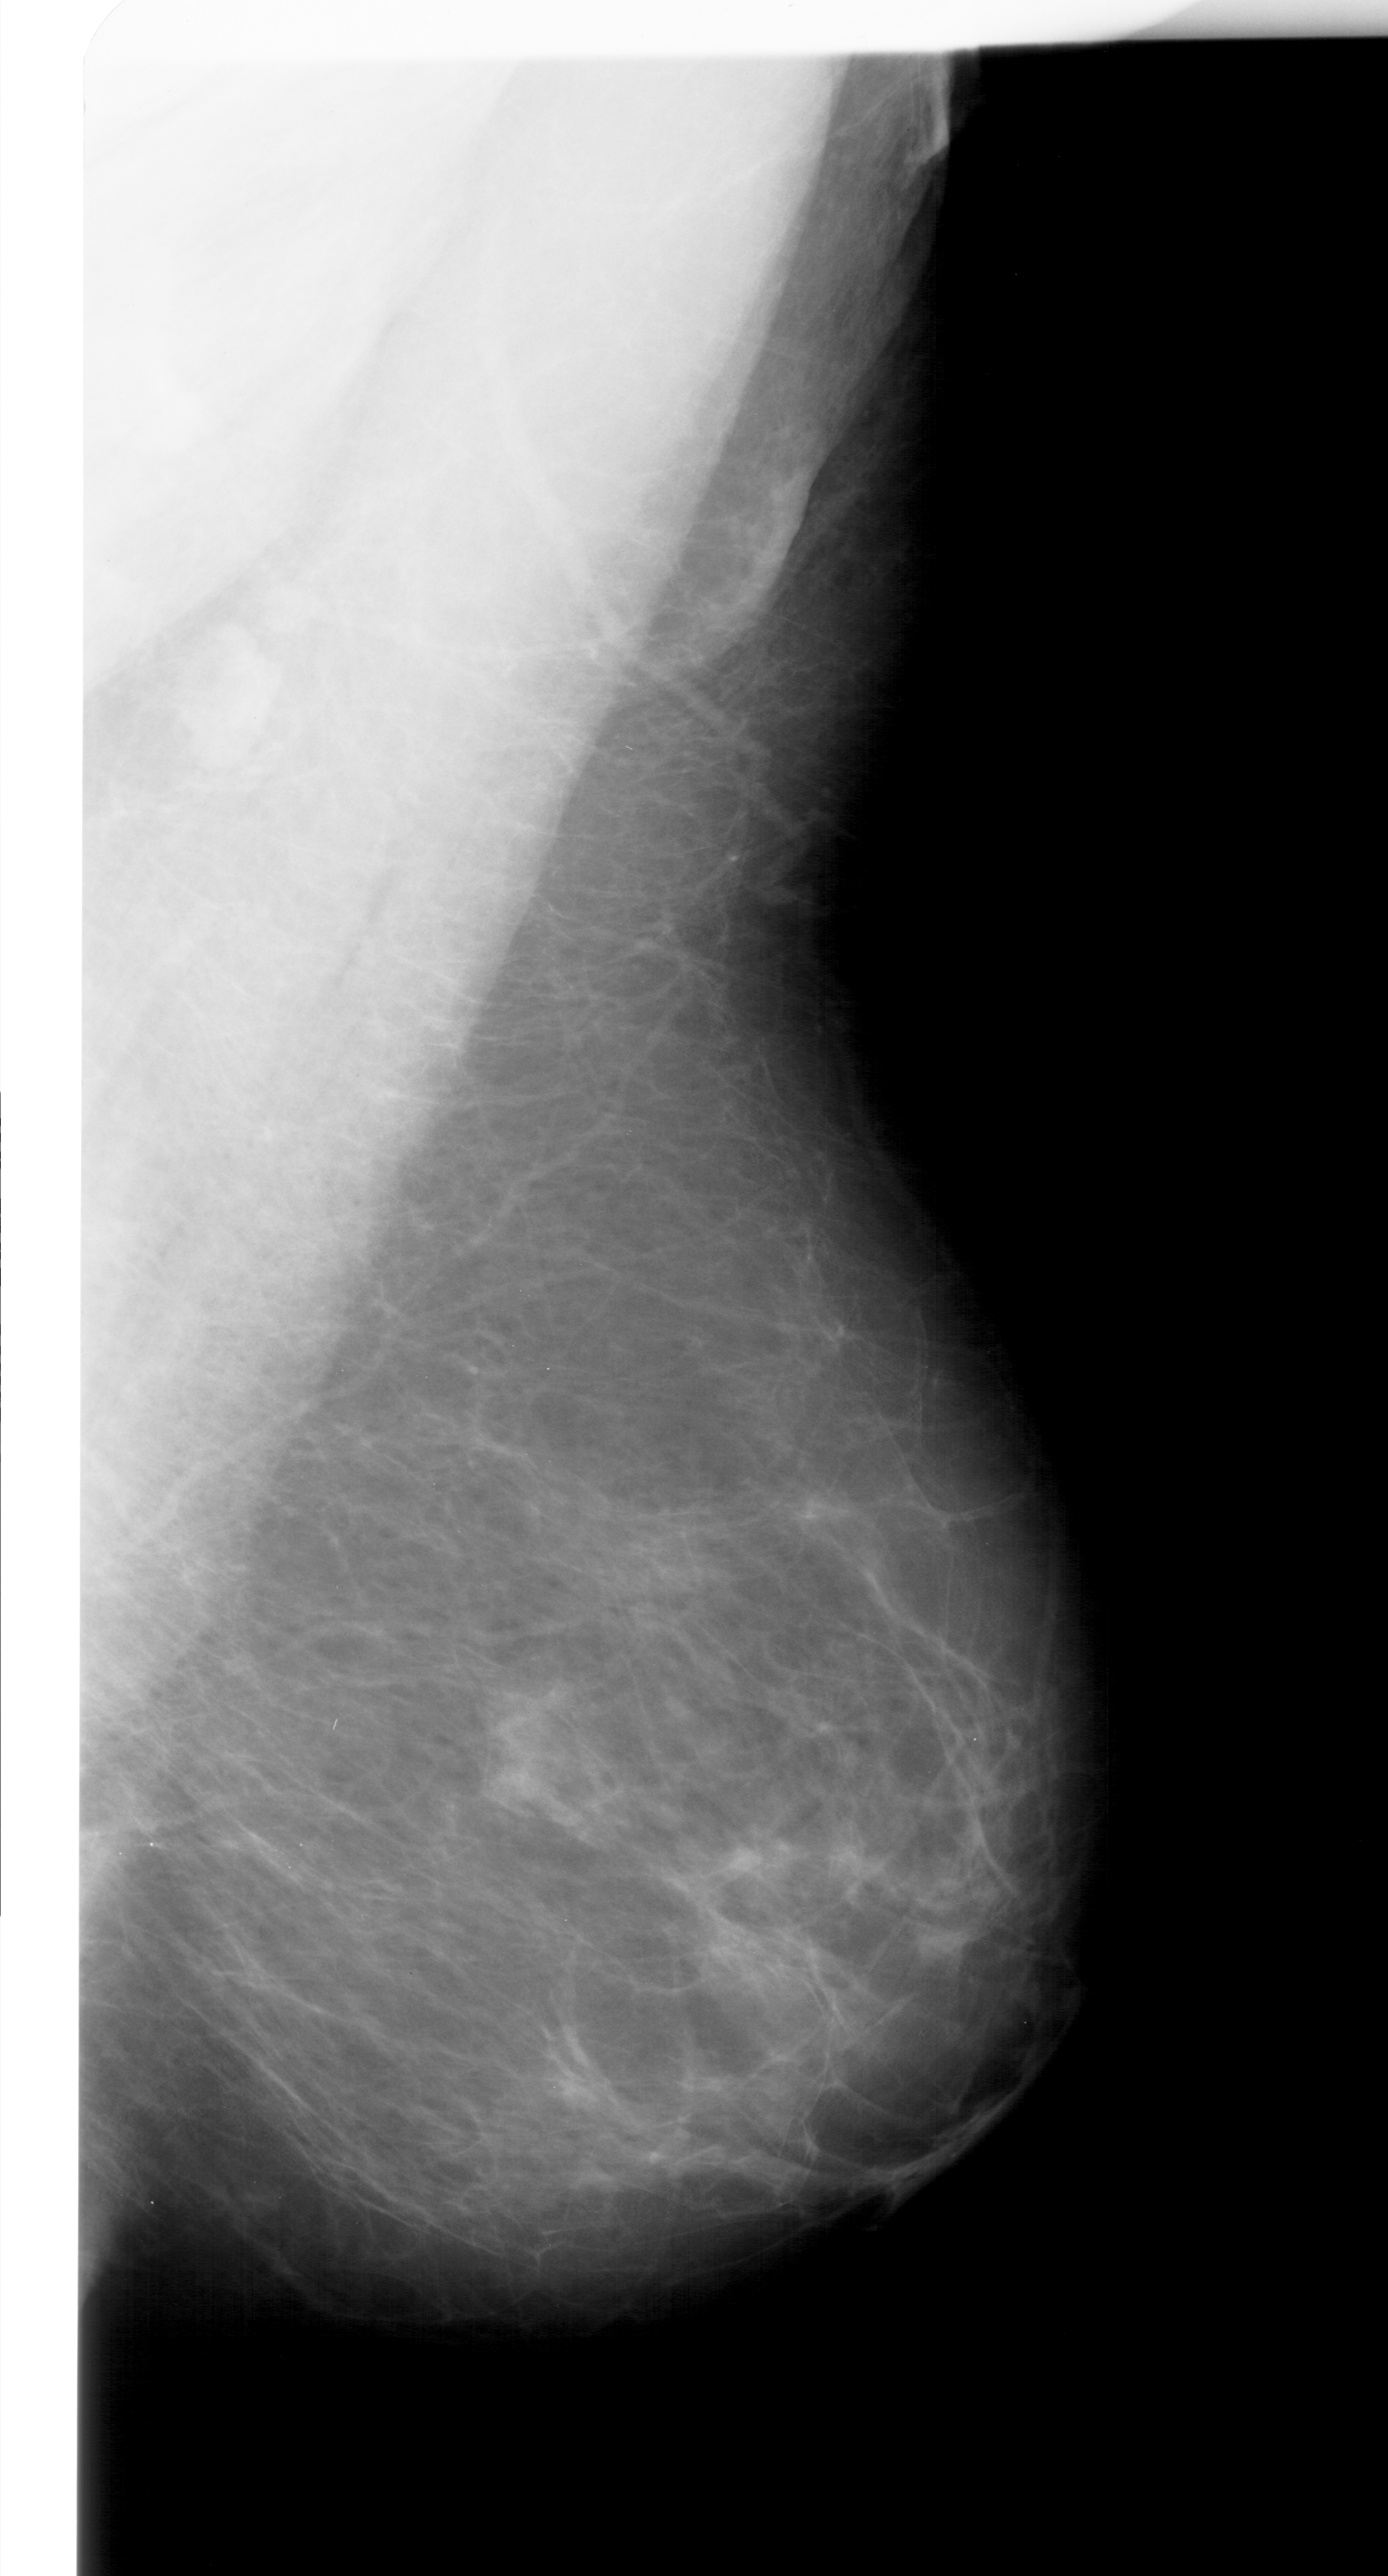
Digitized screen-film mammogram; right breast; MLO view; breast composition: scattered fibroglandular densities (BI-RADS density category 2 of 4); 1388 × 2576 image matrix.
Expert-marked regions of interest on this film, with their recorded descriptors:
- mass, shape focal asymmetric density, margins ill defined; BI-RADS assessment category 4; pathology result (as recorded, not read from the image): benign: bounding box (x1, y1, x2, y2) in pixels: (481, 1684, 571, 1803)